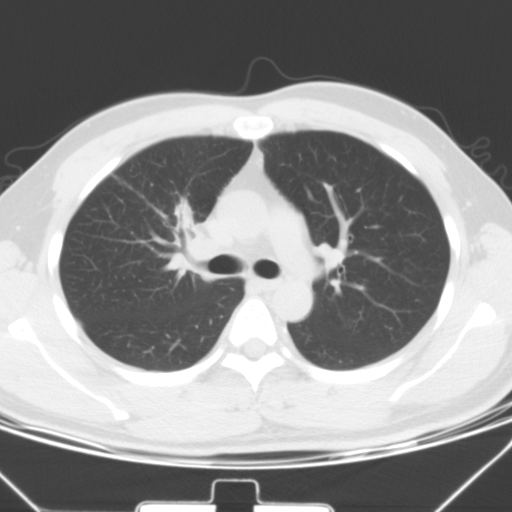
Chest CT, one axial slice; slice 39 of 60 in the series (ordered by position); 120 kVp; lung window (W 1500 / L -600 HU); 5 mm slice thickness; 512 × 512 image matrix, field of view 337 × 337 mm. Male patient, age 35 years. From the clinical record (not read from this slice): clinical TNM (as recorded): T1c N1 M1b.
Structures marked on this image (rectangle marked by the reading radiologist):
- lung tumour (recorded histology: adenocarcinoma): box from (x=171, y=198) to (x=223, y=270) px